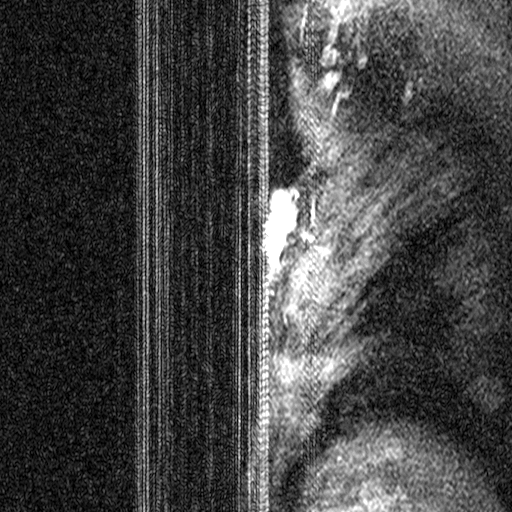
Breast MRI (dynamic contrast-enhanced), one sagittal slice; position 33 of 44 along the scan axis; dynamic contrast-enhanced study with each time point stored as its own series, time point 2 of 3 at this slice position (early post-contrast, ordered by acquisition time); 1.5 T; TE 4.5 ms, TR 11 ms; 512 × 512 image matrix, field of view 200 × 200 mm. Female patient, age 44 years. From the clinical record (not read from this slice): setting: breast cancer imaged before/during neoadjuvant chemotherapy; receptor status: HR-positive, HER2-negative.
Outlined on this slice (semi-automatic segmentation, software-assisted and operator-edited):
- analysis volume of interest (the breast-tissue region the enhancement analysis was run in; not a lesion): bounding box (x1, y1, x2, y2) in pixels: (206, 164, 319, 299)
- tumour enhancement mask (voxels above the 90 % enhancement threshold inside the analysis volume of interest): (259, 164, 314, 266)